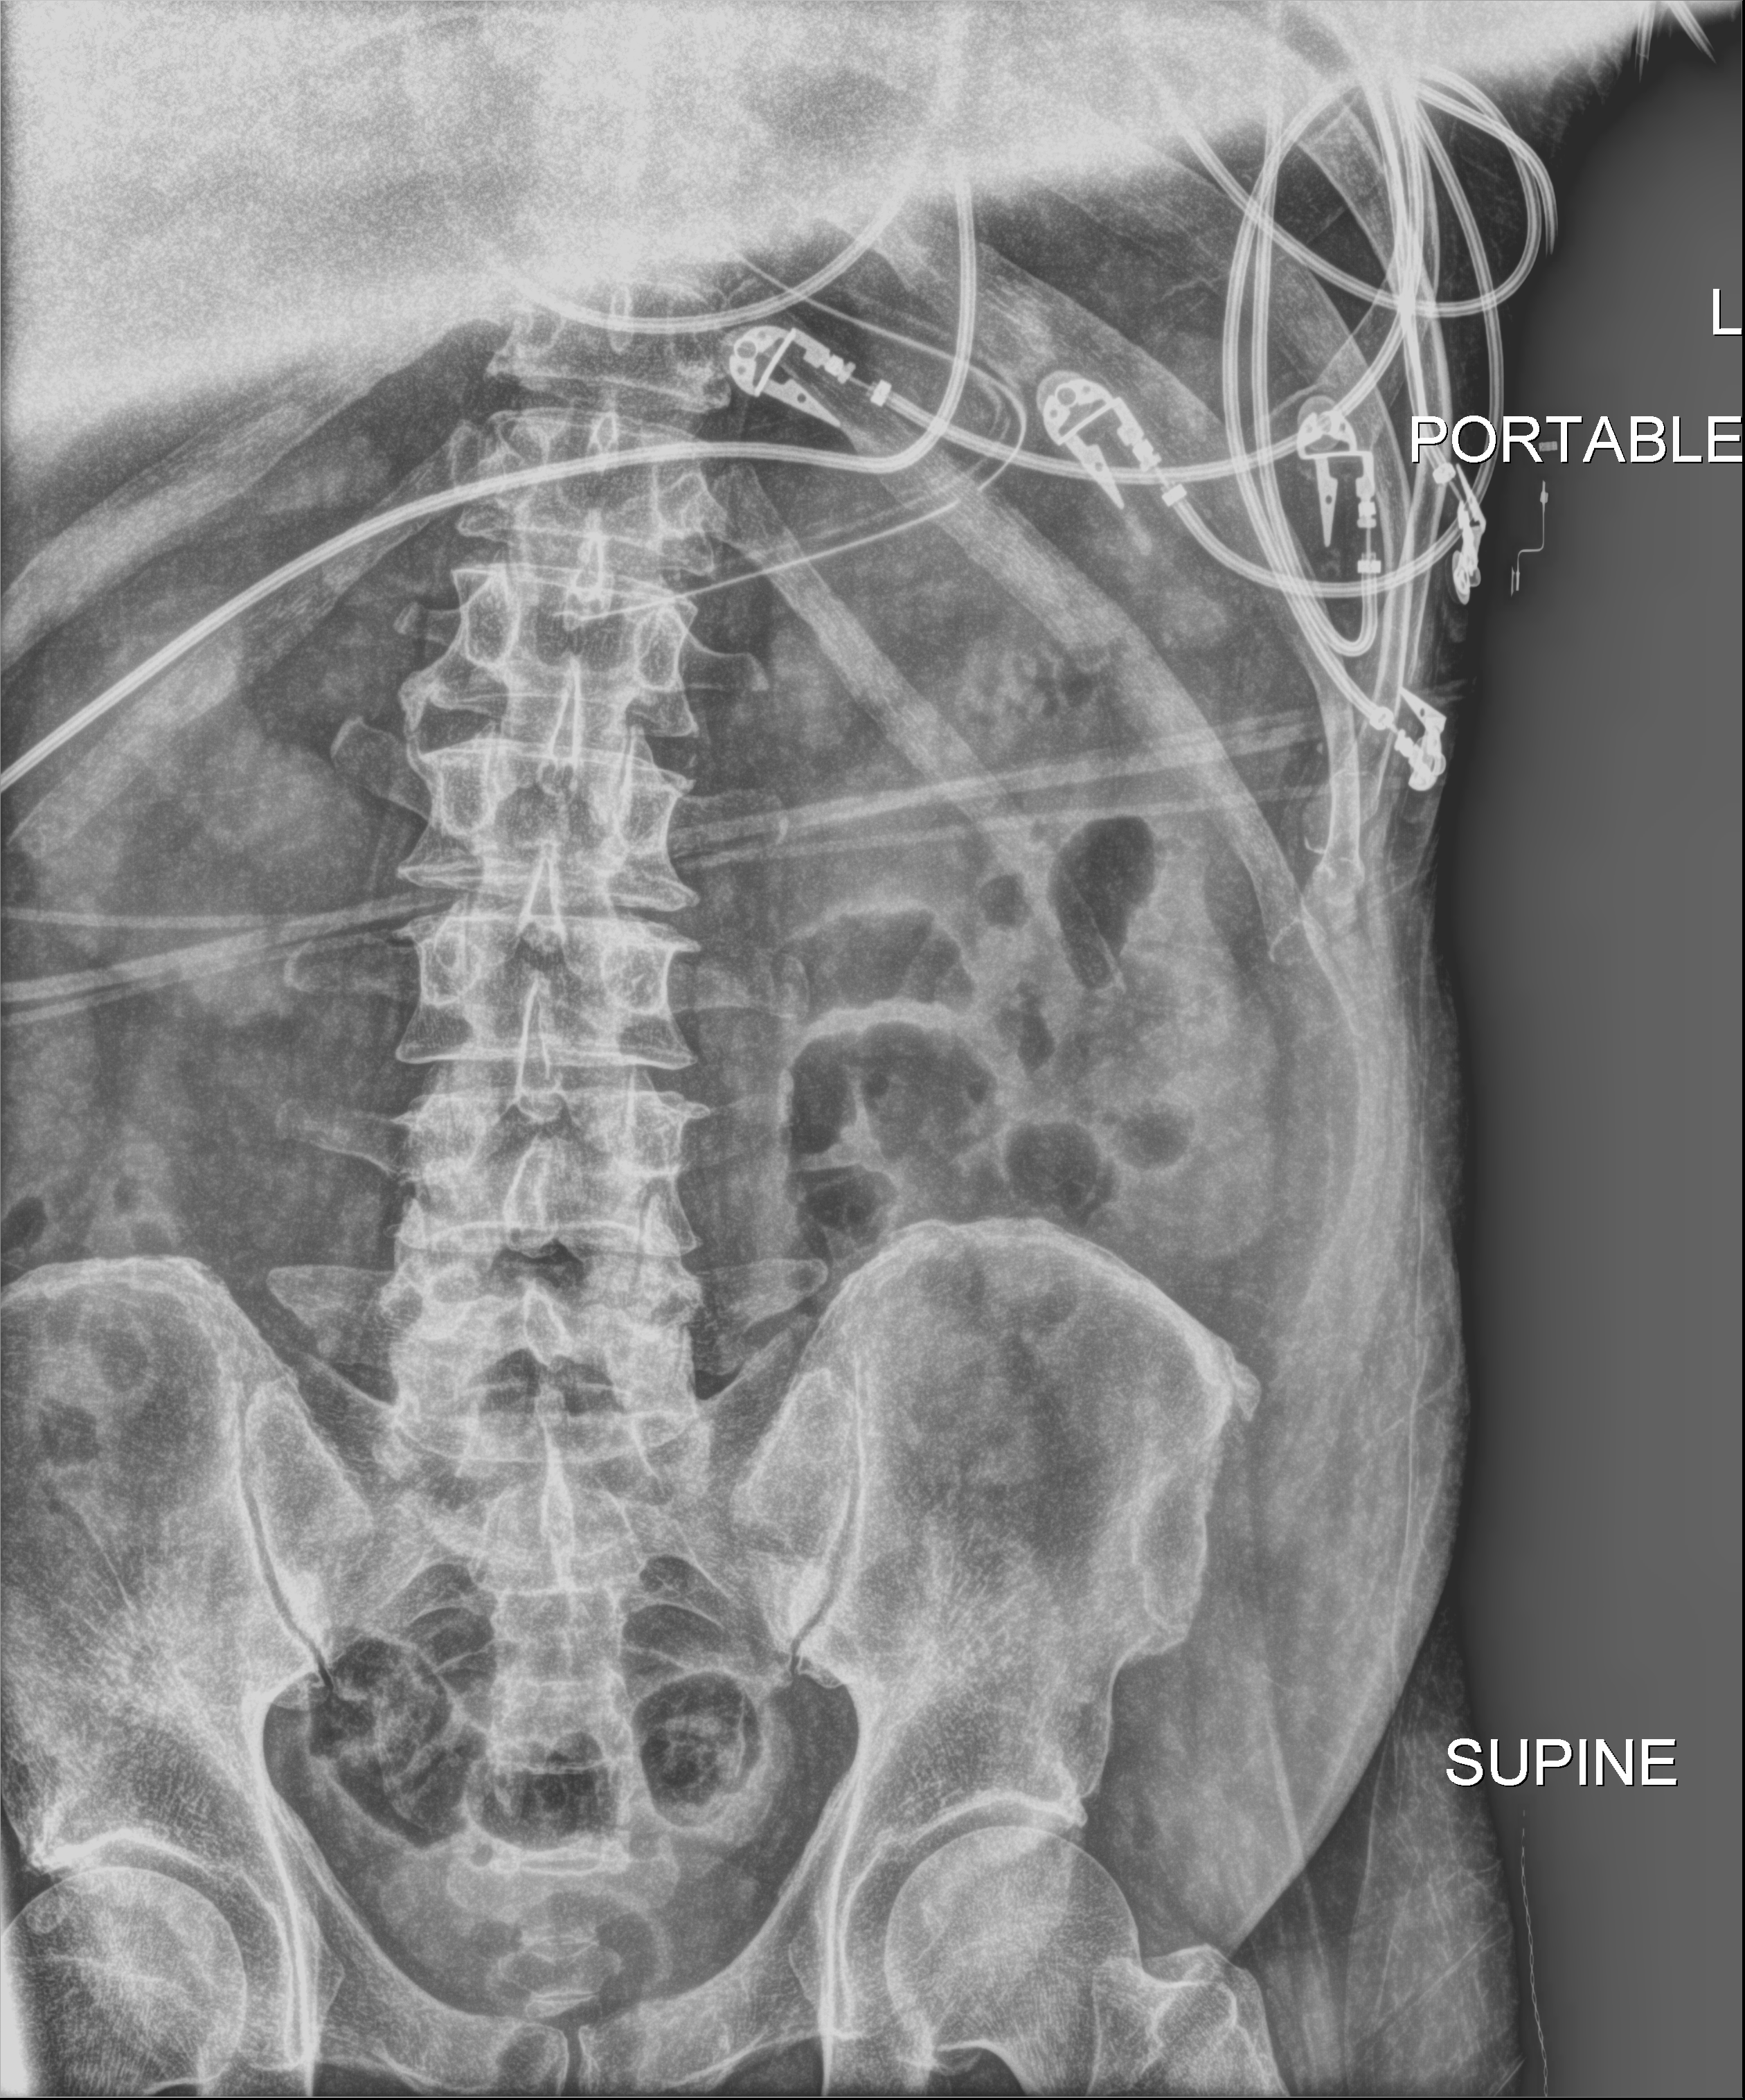
Abdomen X-ray (portable). Patient hospitalised with COVID-19; male, aged 18–59 years.
Admission-level facts for this patient (not findings on this image; timing relative to this image not recorded): admitted to intensive care during this hospital stay: yes; COPD (admission record): no; mechanically ventilated during this hospital stay: yes.